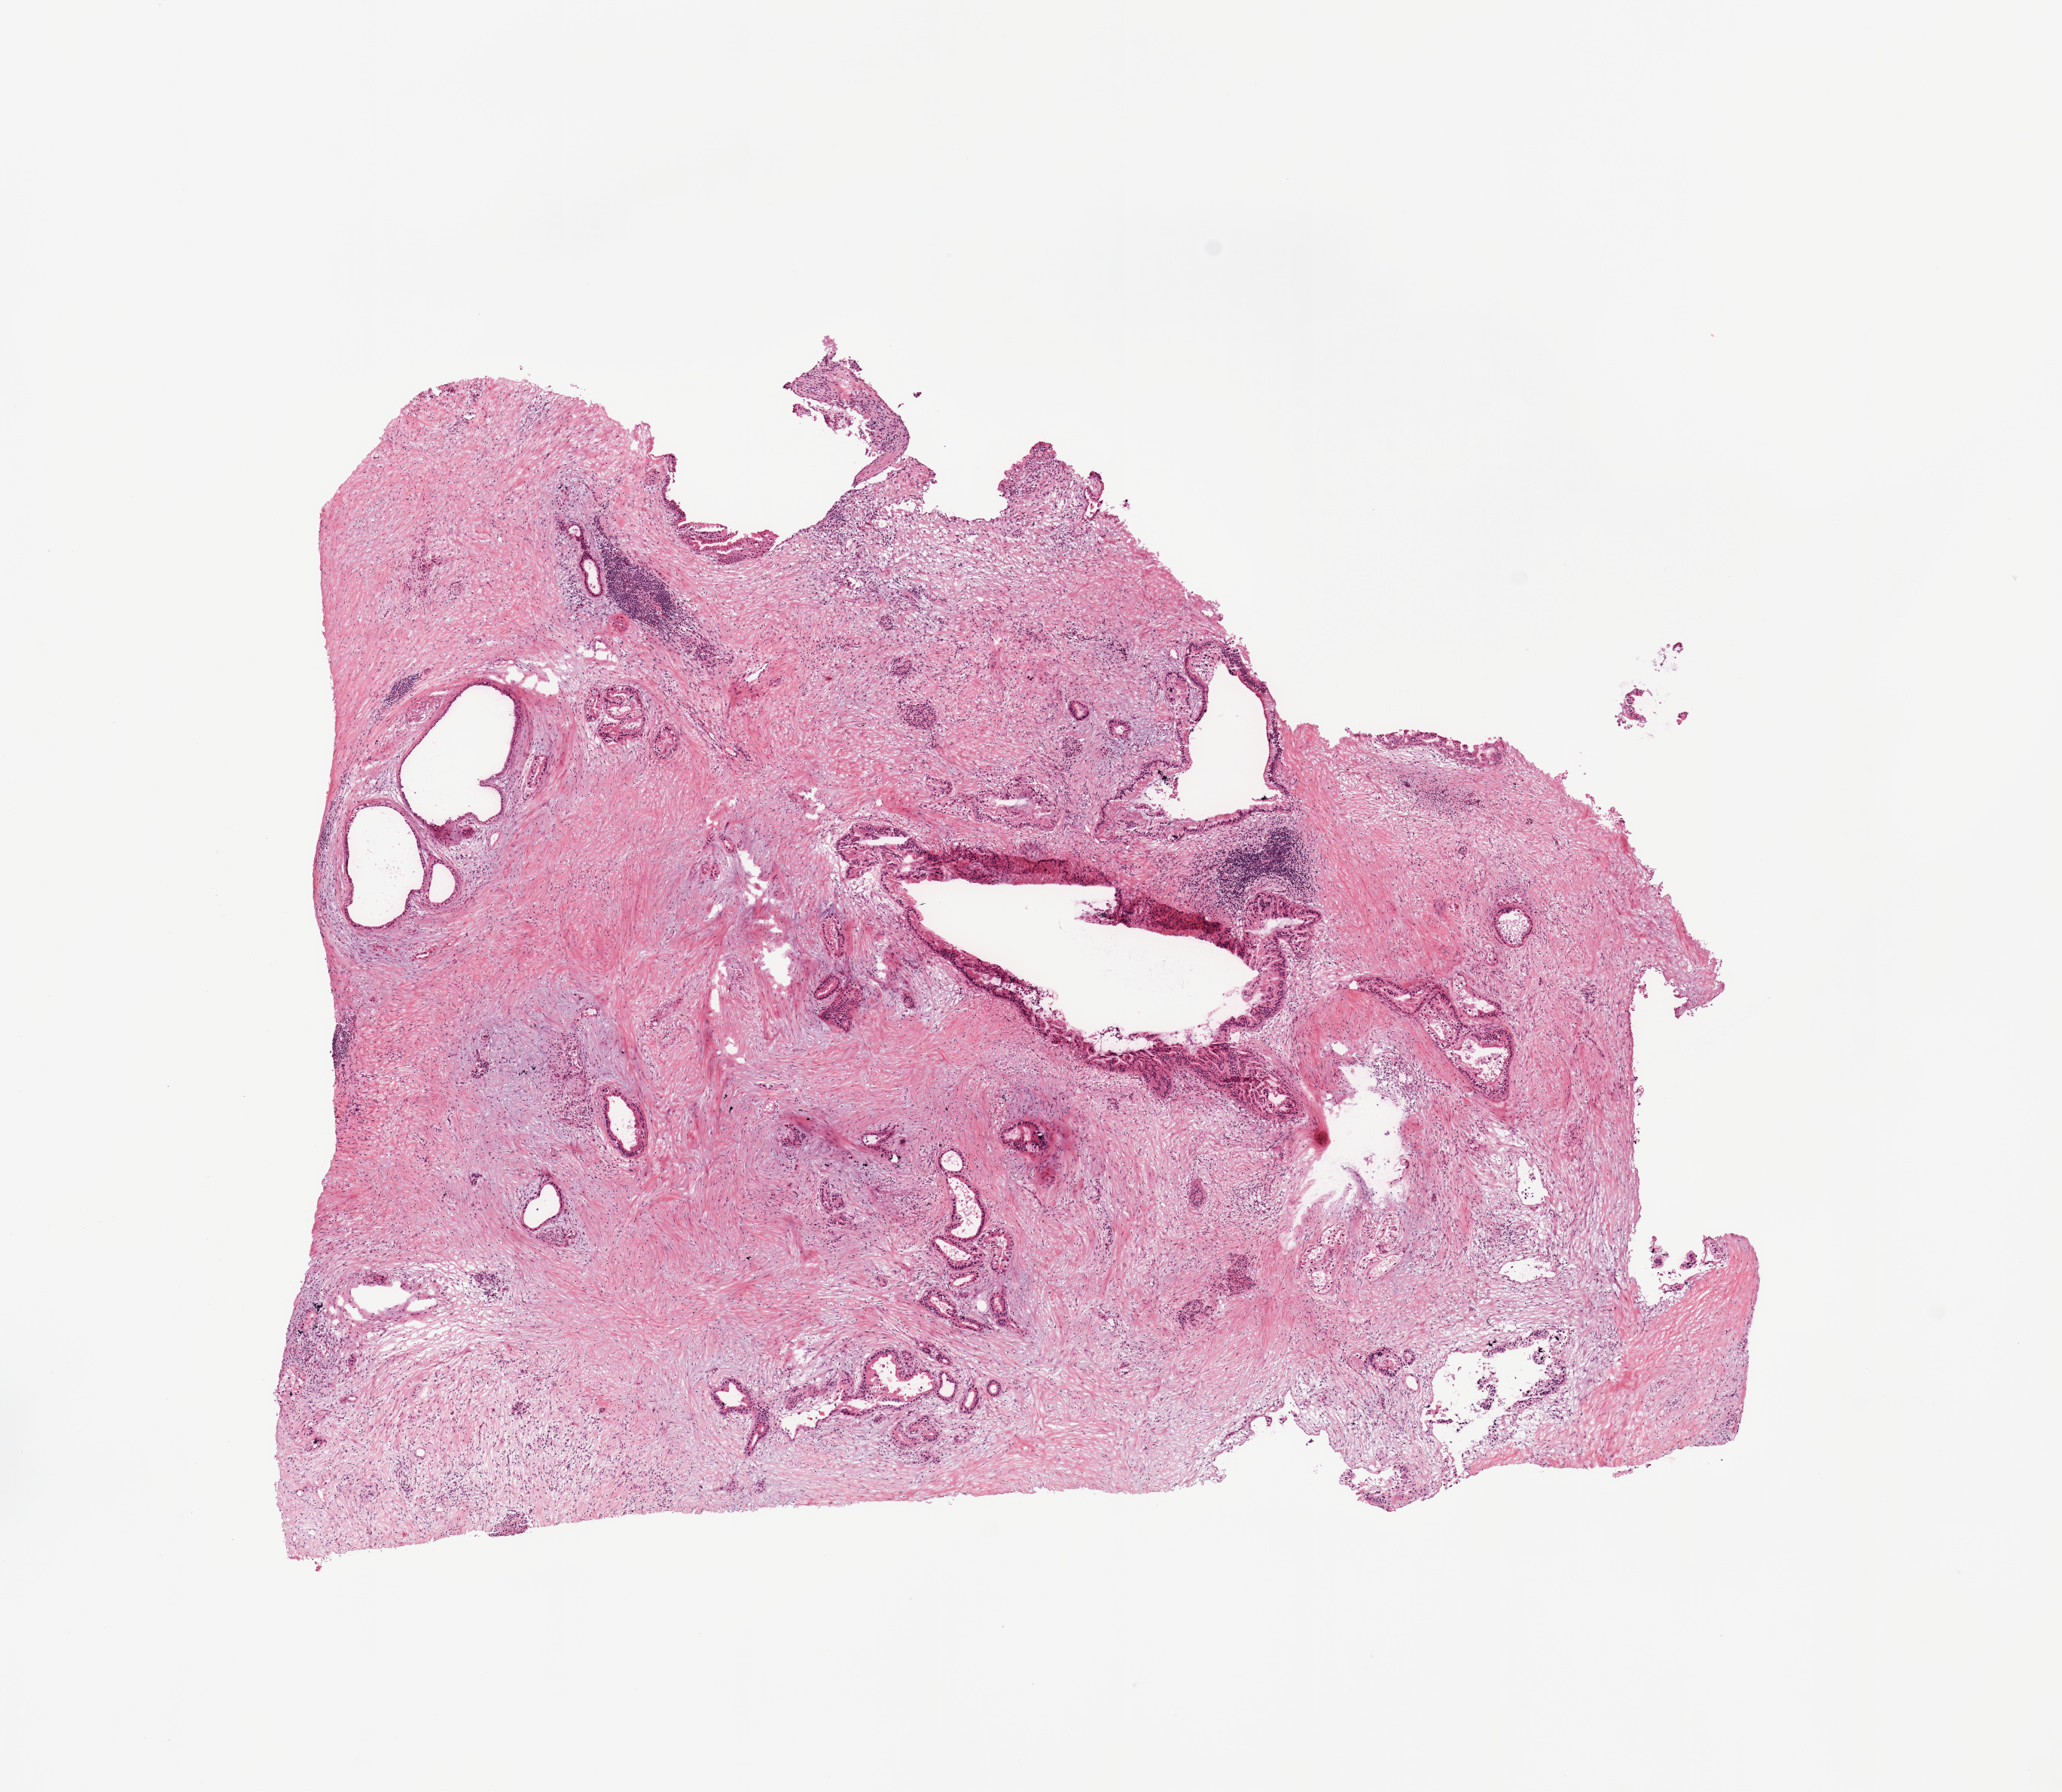
Whole-slide histology image, H&E-stained — a low-resolution overview of the entire scanned area, about 10.8 x 9.4 mm (from a 20x scan); tumour tissue sample, sampled site: pancreas. Male, 69 y/o. Histologic grade: G2 (moderately differentiated). Composition of this section per pathologist review: tumour nuclei 20%, necrosis 0%.
- histologic diagnosis: Infiltrating duct carcinoma, NOS
- AJCC pathologic stage: IIA
- primary tumour site (as recorded): head